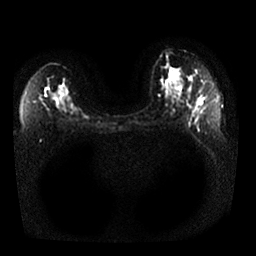
Breast MRI, one axial slice; slice 18 of 25 in the series (ordered by position); diffusion-weighted series; image 2 of 4 stored at this slice position (different b-values; order by instance number); 1.5 T; 4 mm slice thickness; 256 × 256 image matrix, field of view 350 × 350 mm. Female patient.
Annotated regions visible in this slice (expert manual segmentation):
- tumour on diffusion-weighted imaging: box from (x=200, y=98) to (x=204, y=104) px